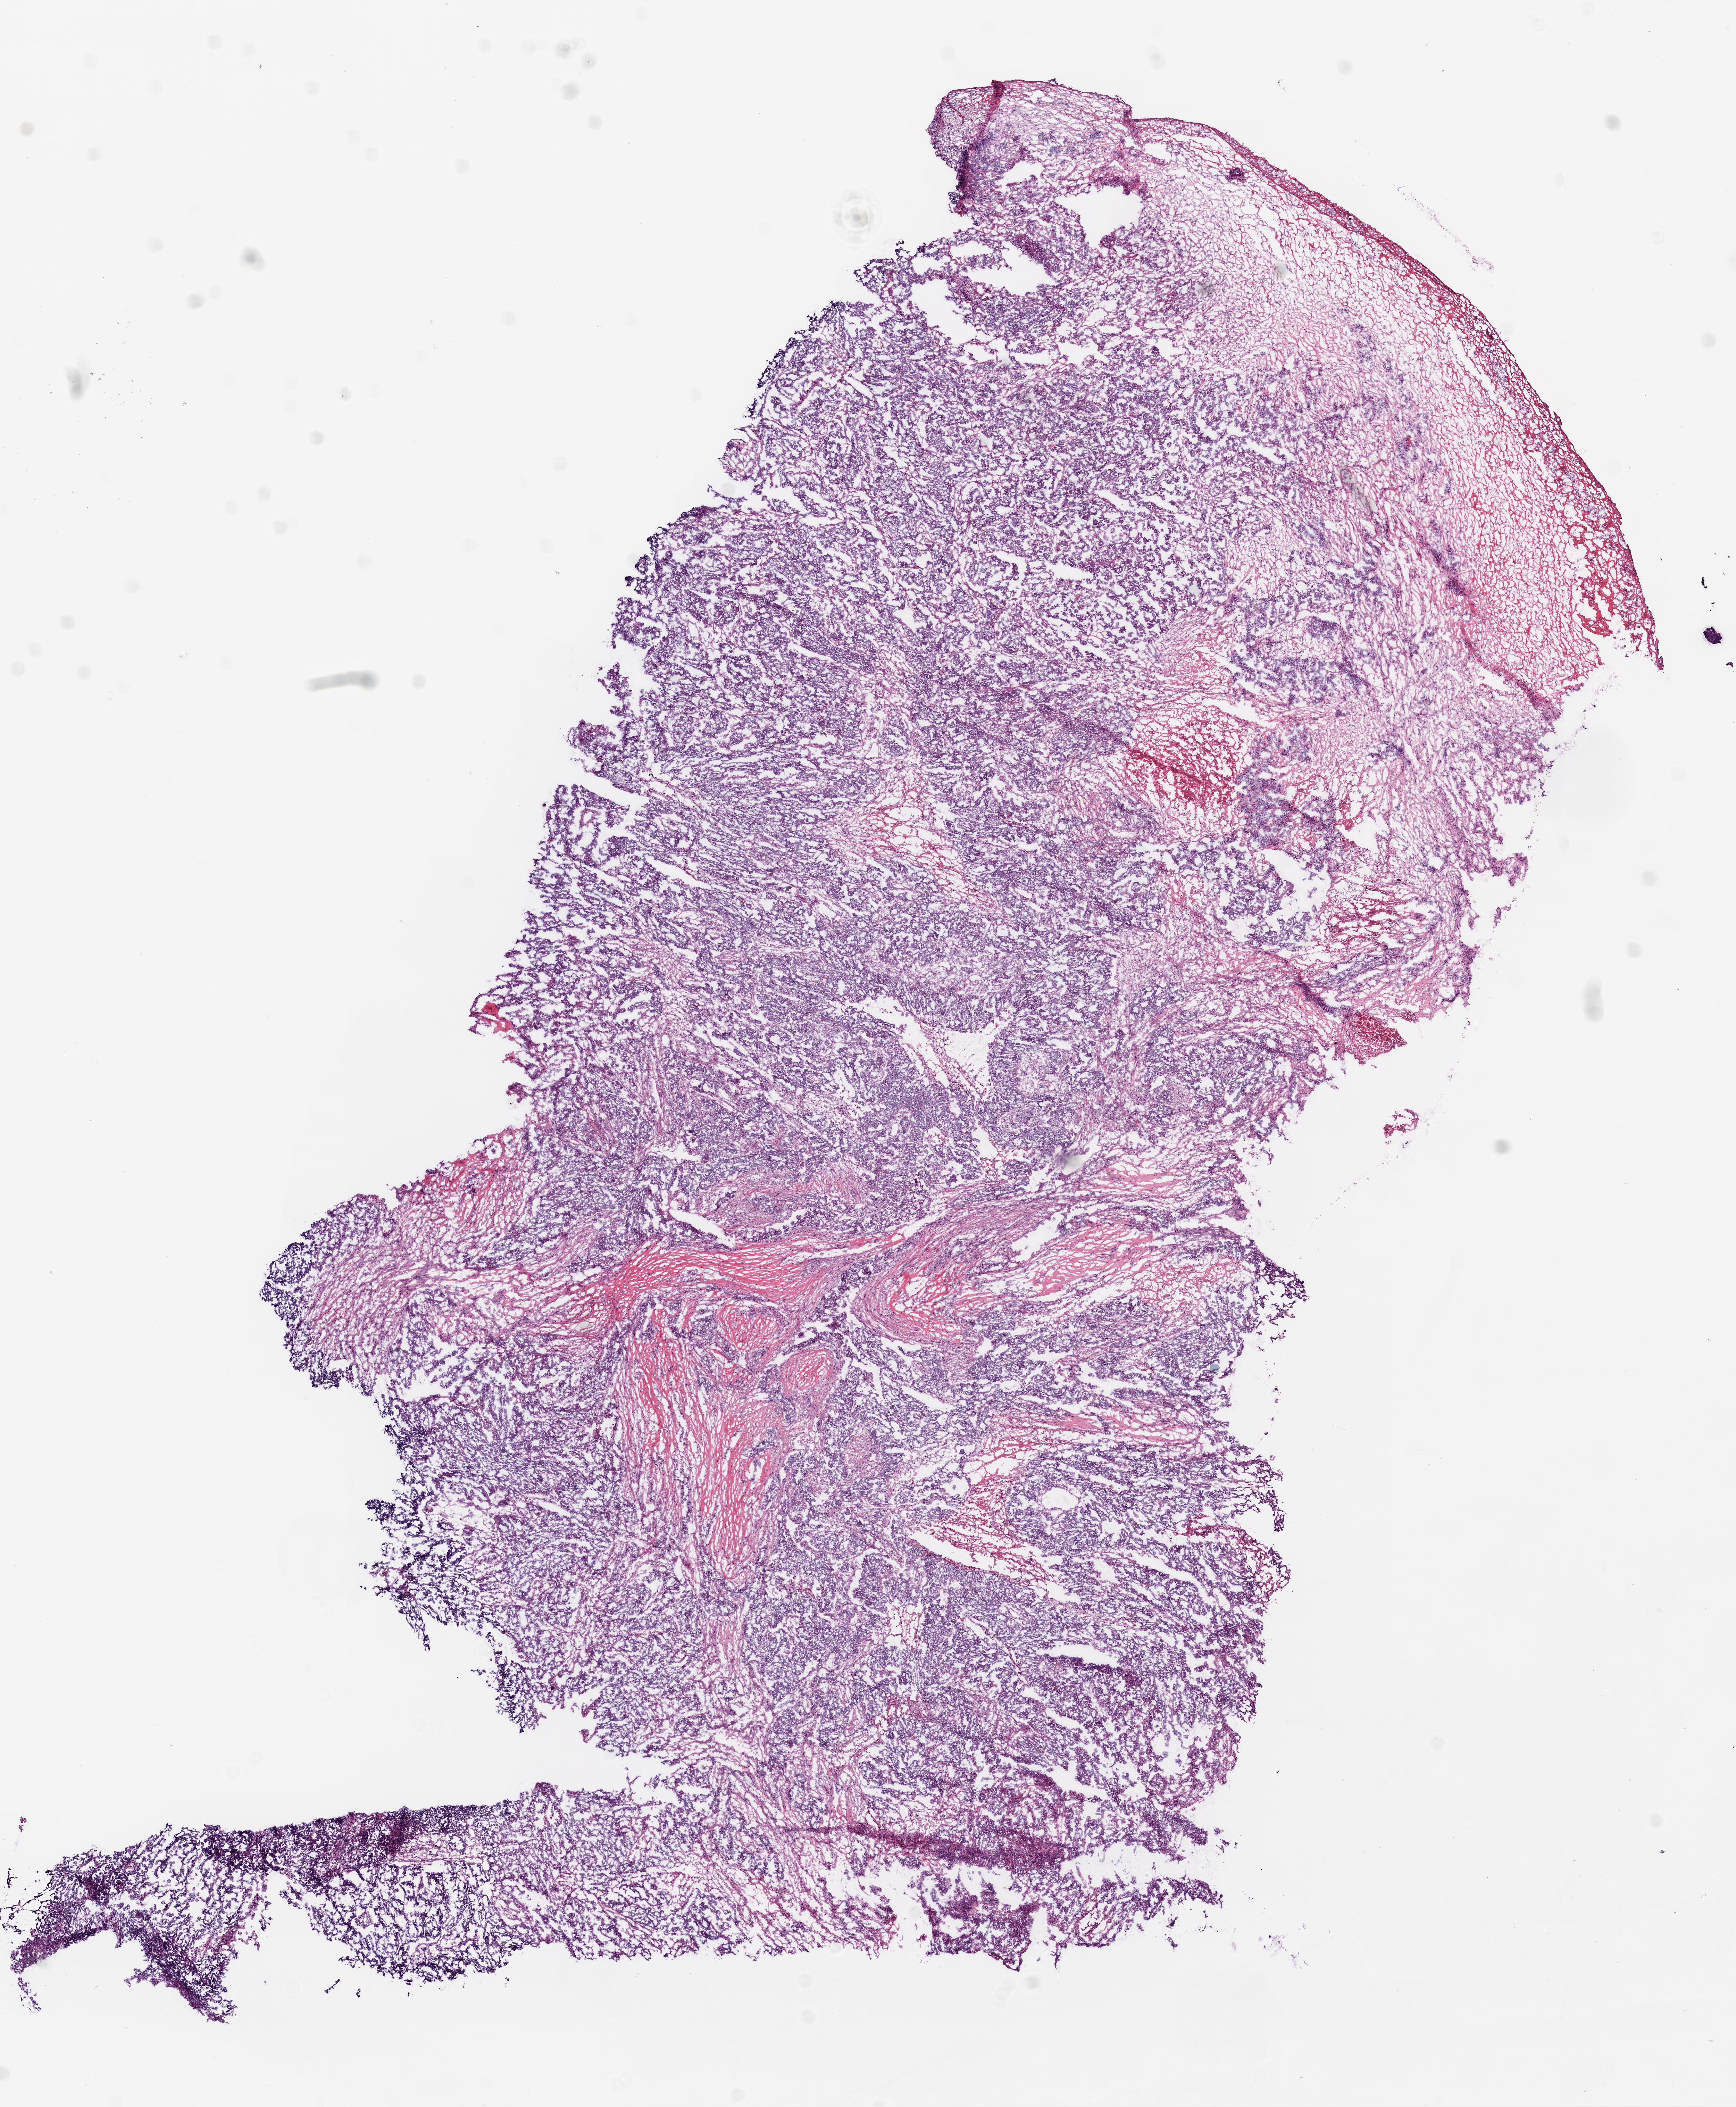
Whole-slide histology image, Hematoxylin and eosin (H&E) stained, a low-resolution overview of the entire scanned area, about 10.0 x 12.2 mm (slide scanned at 20x). Frozen section from the bottom of the tissue portion. Primary tumour sample from the ovary. Female, age 49 years at initial diagnosis. Histologic grade: G3 (poorly differentiated). Pathologist review of this section (percent, as recorded): tumour cells 100%, tumour nuclei 80%, normal cells 0%, stromal cells 0%, necrosis 0%.
- laterality: bilateral
- diagnosis: Serous cystadenocarcinoma, NOS
- FIGO stage: IIIC